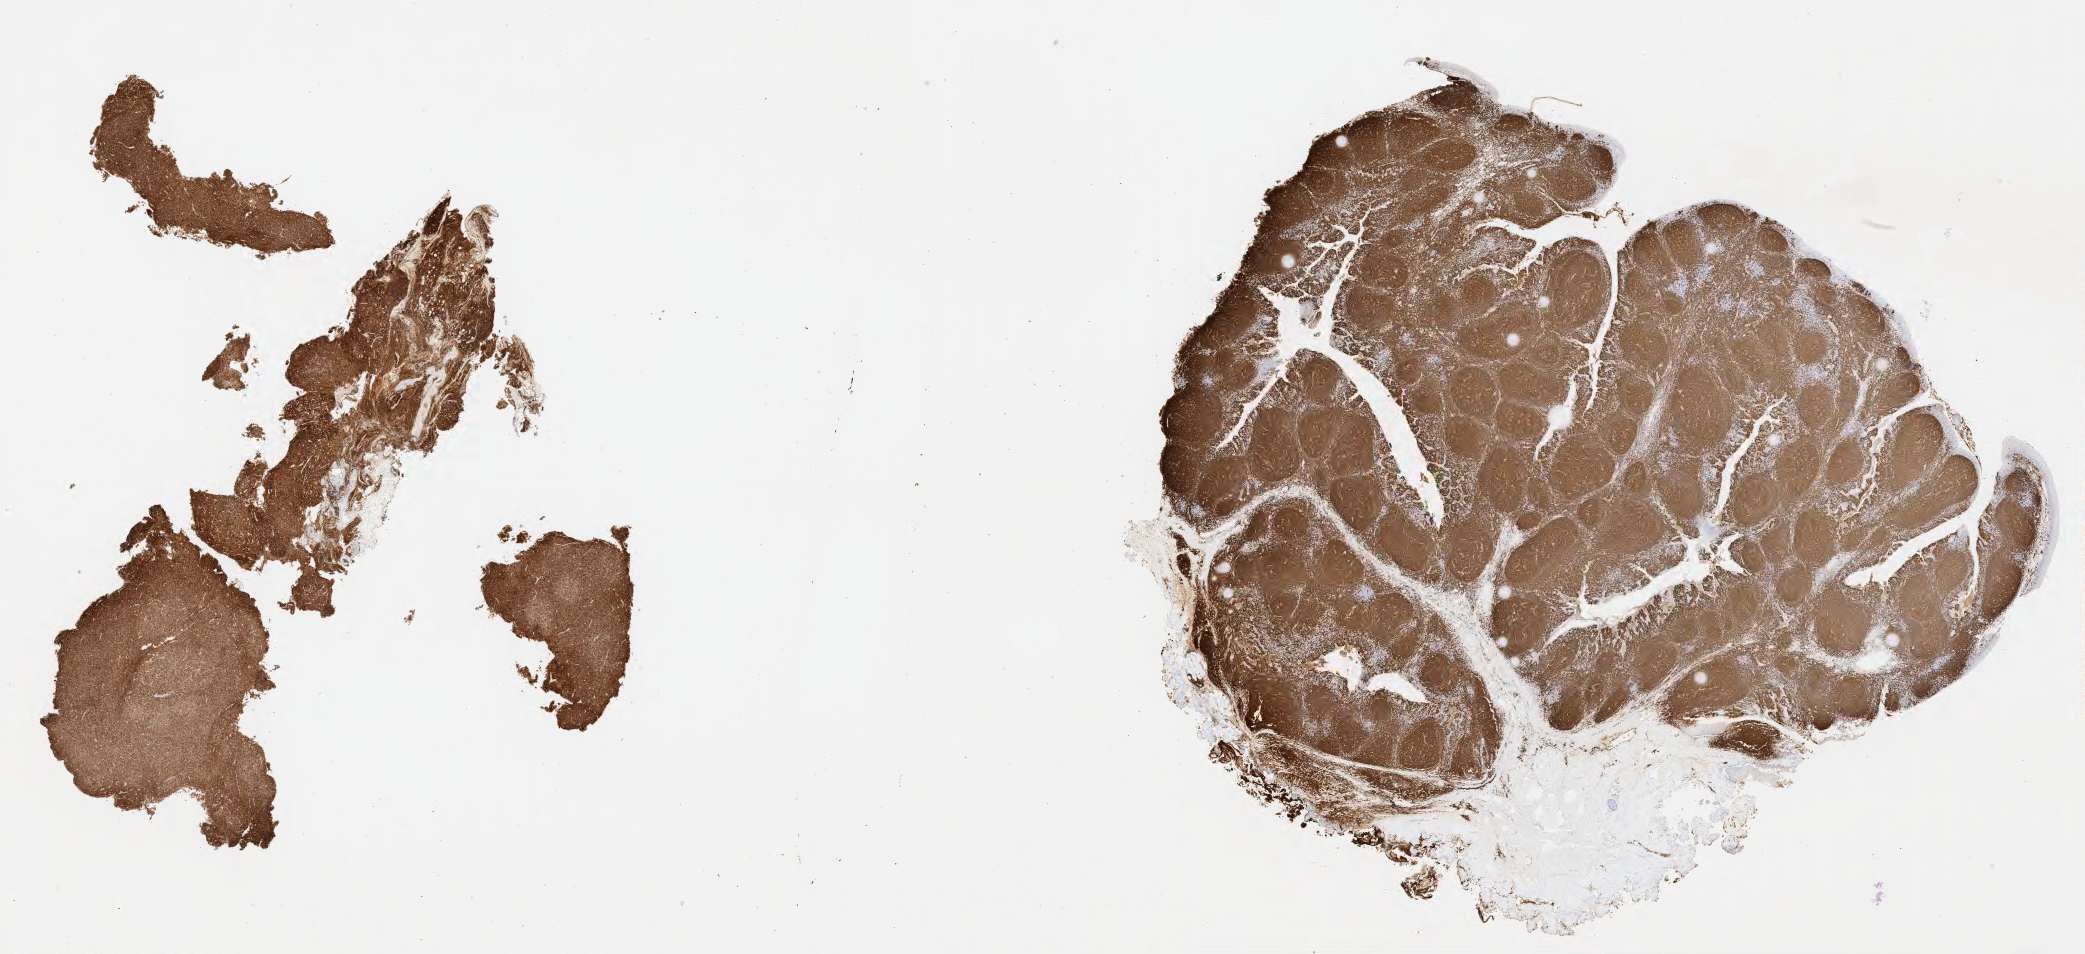
Whole-slide image, immunohistochemical stain for CD20, shown as a low-resolution overview of the whole scanned area (about 33.7 x 15.4 mm). Tumor tissue. Site: liver. Patient: female, 36 years old.
Diagnosis: Diffuse large B-cell lymphoma, NOS.